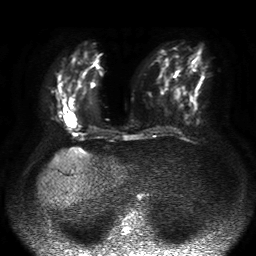
Breast MRI, one axial slice; position 21 of 50 along the scan axis; diffusion-weighted series; image 2 of 4 stored at this slice position (different b-values; order by instance number); 1.5 T; 4 mm slice thickness; 256 × 256 image matrix. Female patient.
Structures marked on this image (expert manual segmentation):
- tumour on diffusion-weighted imaging: bounding box <63,114,77,128> (left, top, right, bottom; pixels)